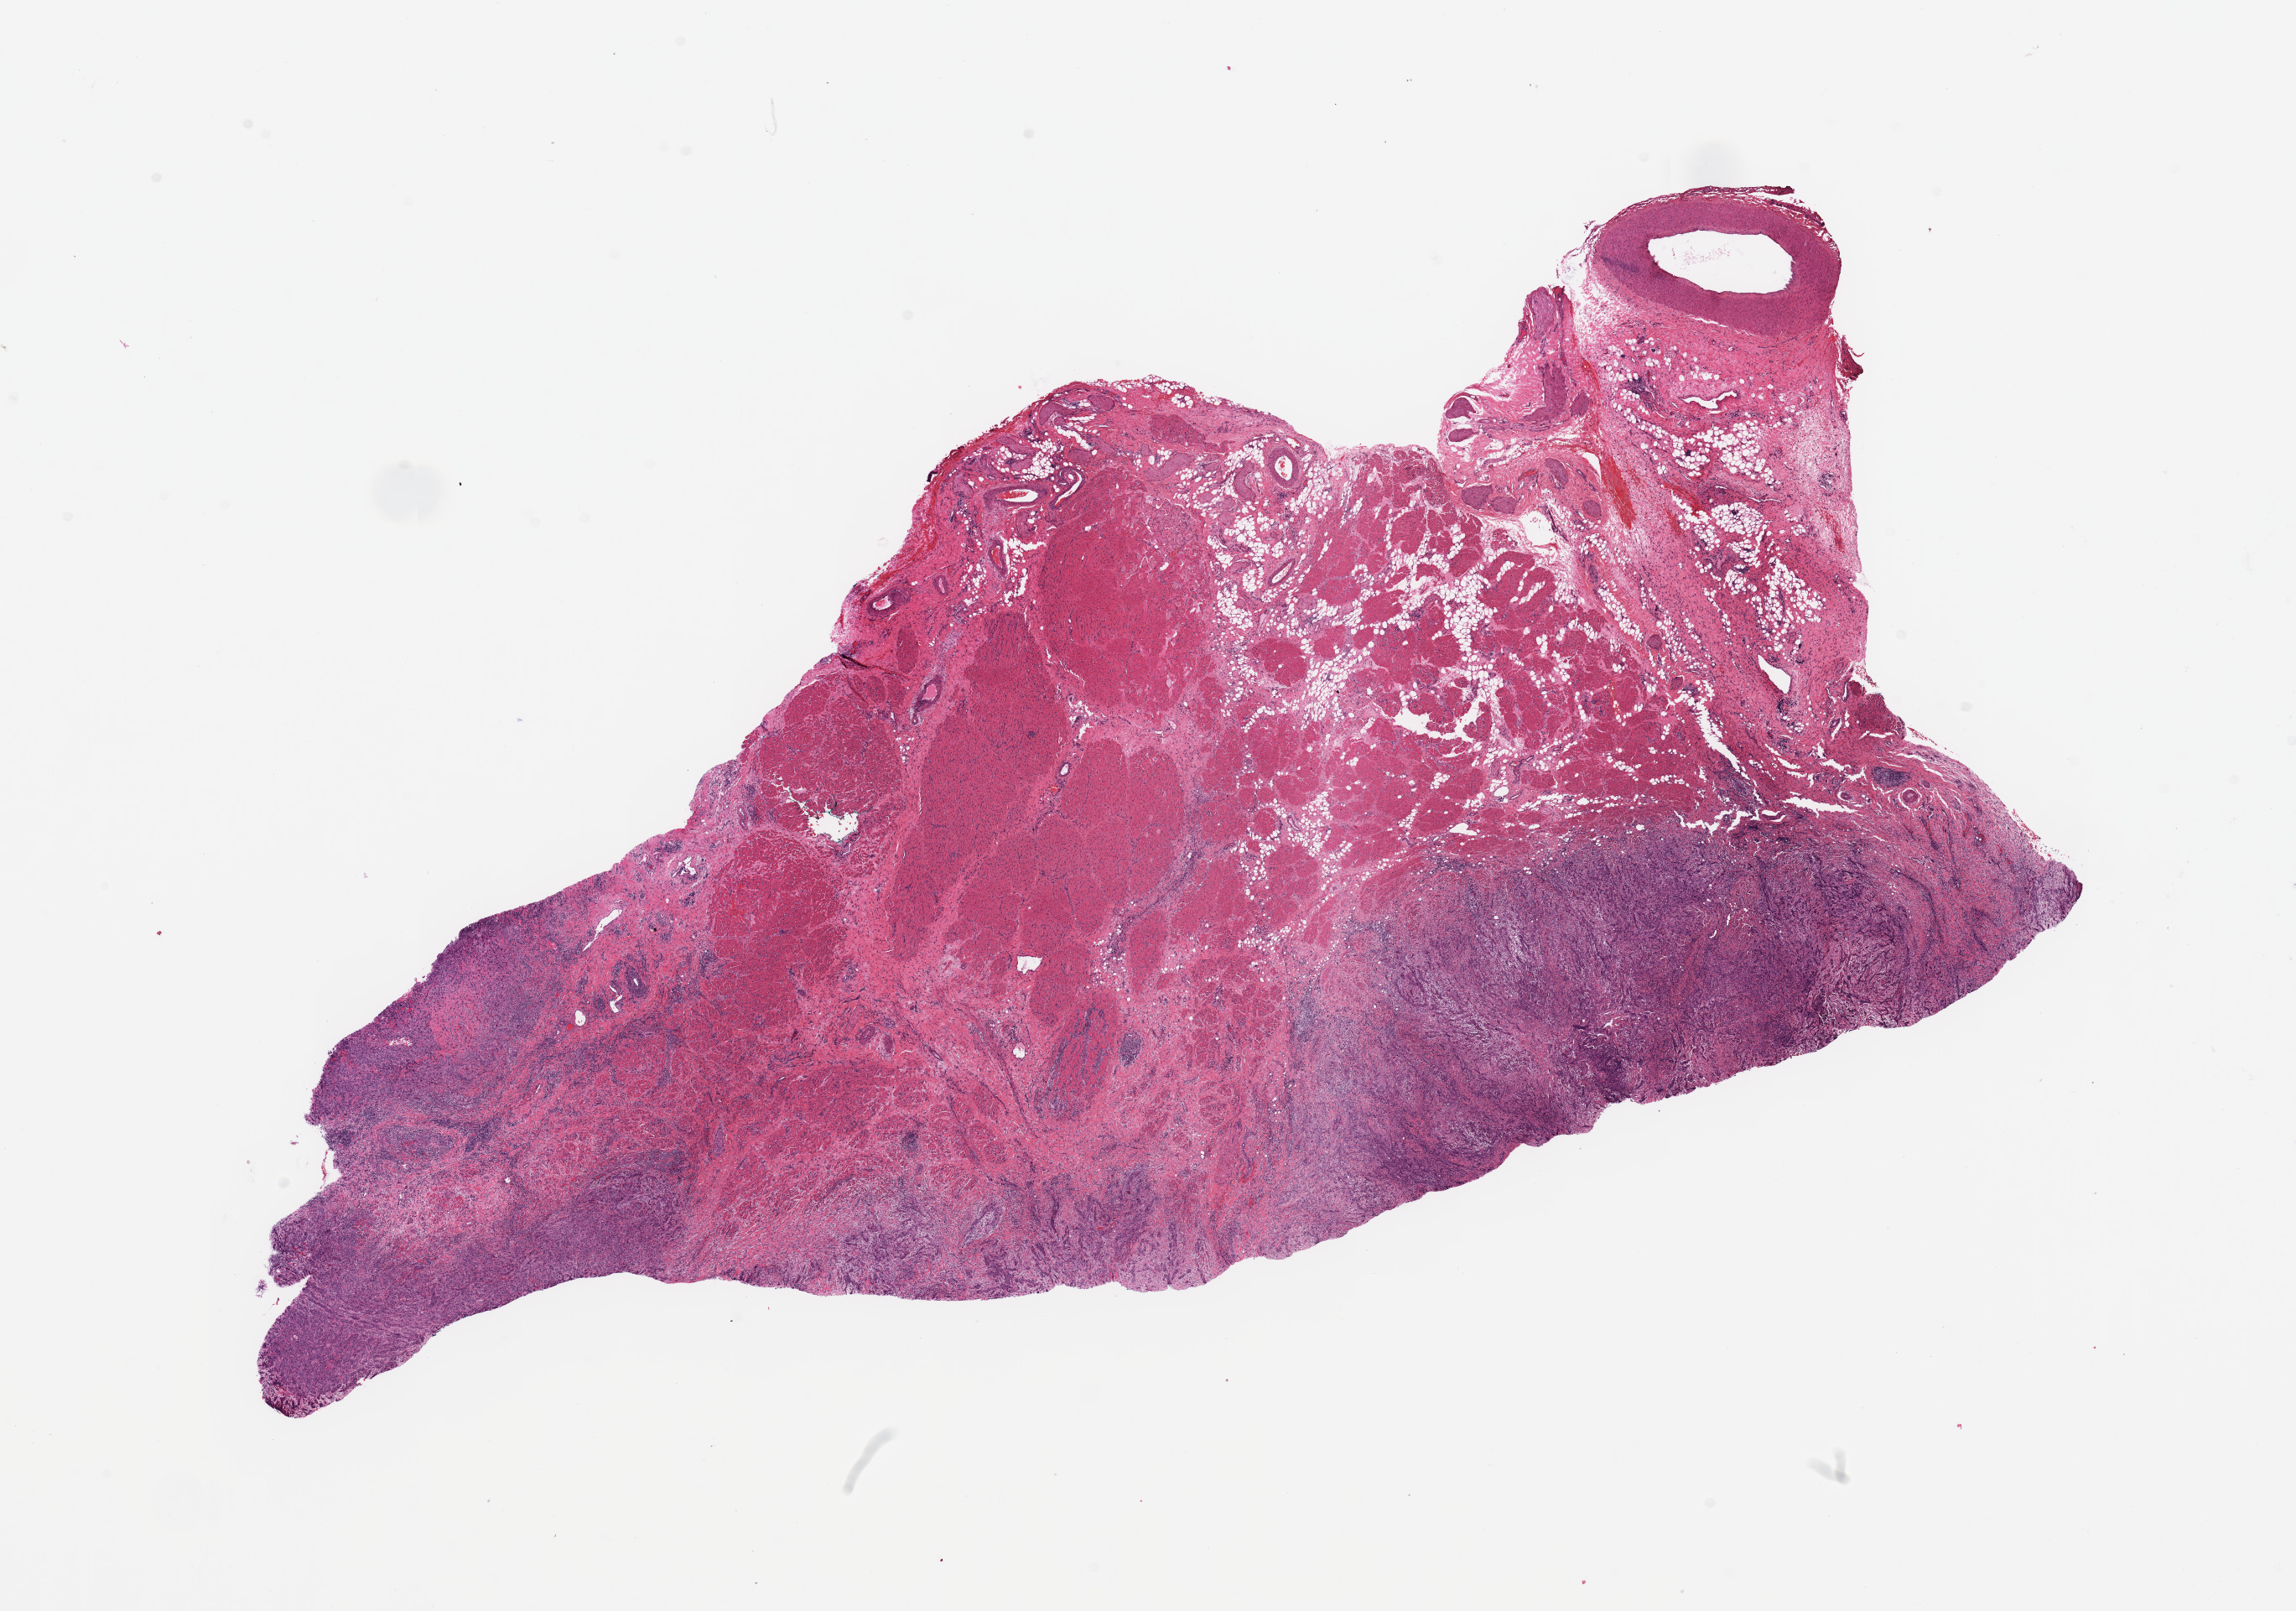
Whole-slide histology image, H&E, shown as a low-resolution overview of the whole scanned area (about 21.7 x 15.2 mm, acquisition: 20x scan); head and neck, tissue type not recorded. Patient: male, age 50 years.
Patient diagnosis: Squamous cell carcinoma, NOS (tongue, NOS).